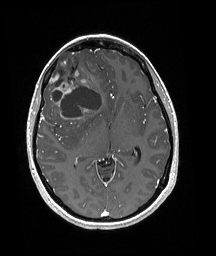
Brain MRI from a brain-tumour surgery series, one axial slice; position 104 of 192 along the scan axis; T1-weighted post-contrast; 1 mm slice thickness; 216 × 256 image matrix. Case-level facts recorded for this patient, not image findings: histopathology: Oligodendroglioma; WHO grade: 3; IDH mutation: yes.
Structures marked on this image (outlined manually by an expert reader):
- tumour: bounding box <49,52,102,119> (left, top, right, bottom; pixels)